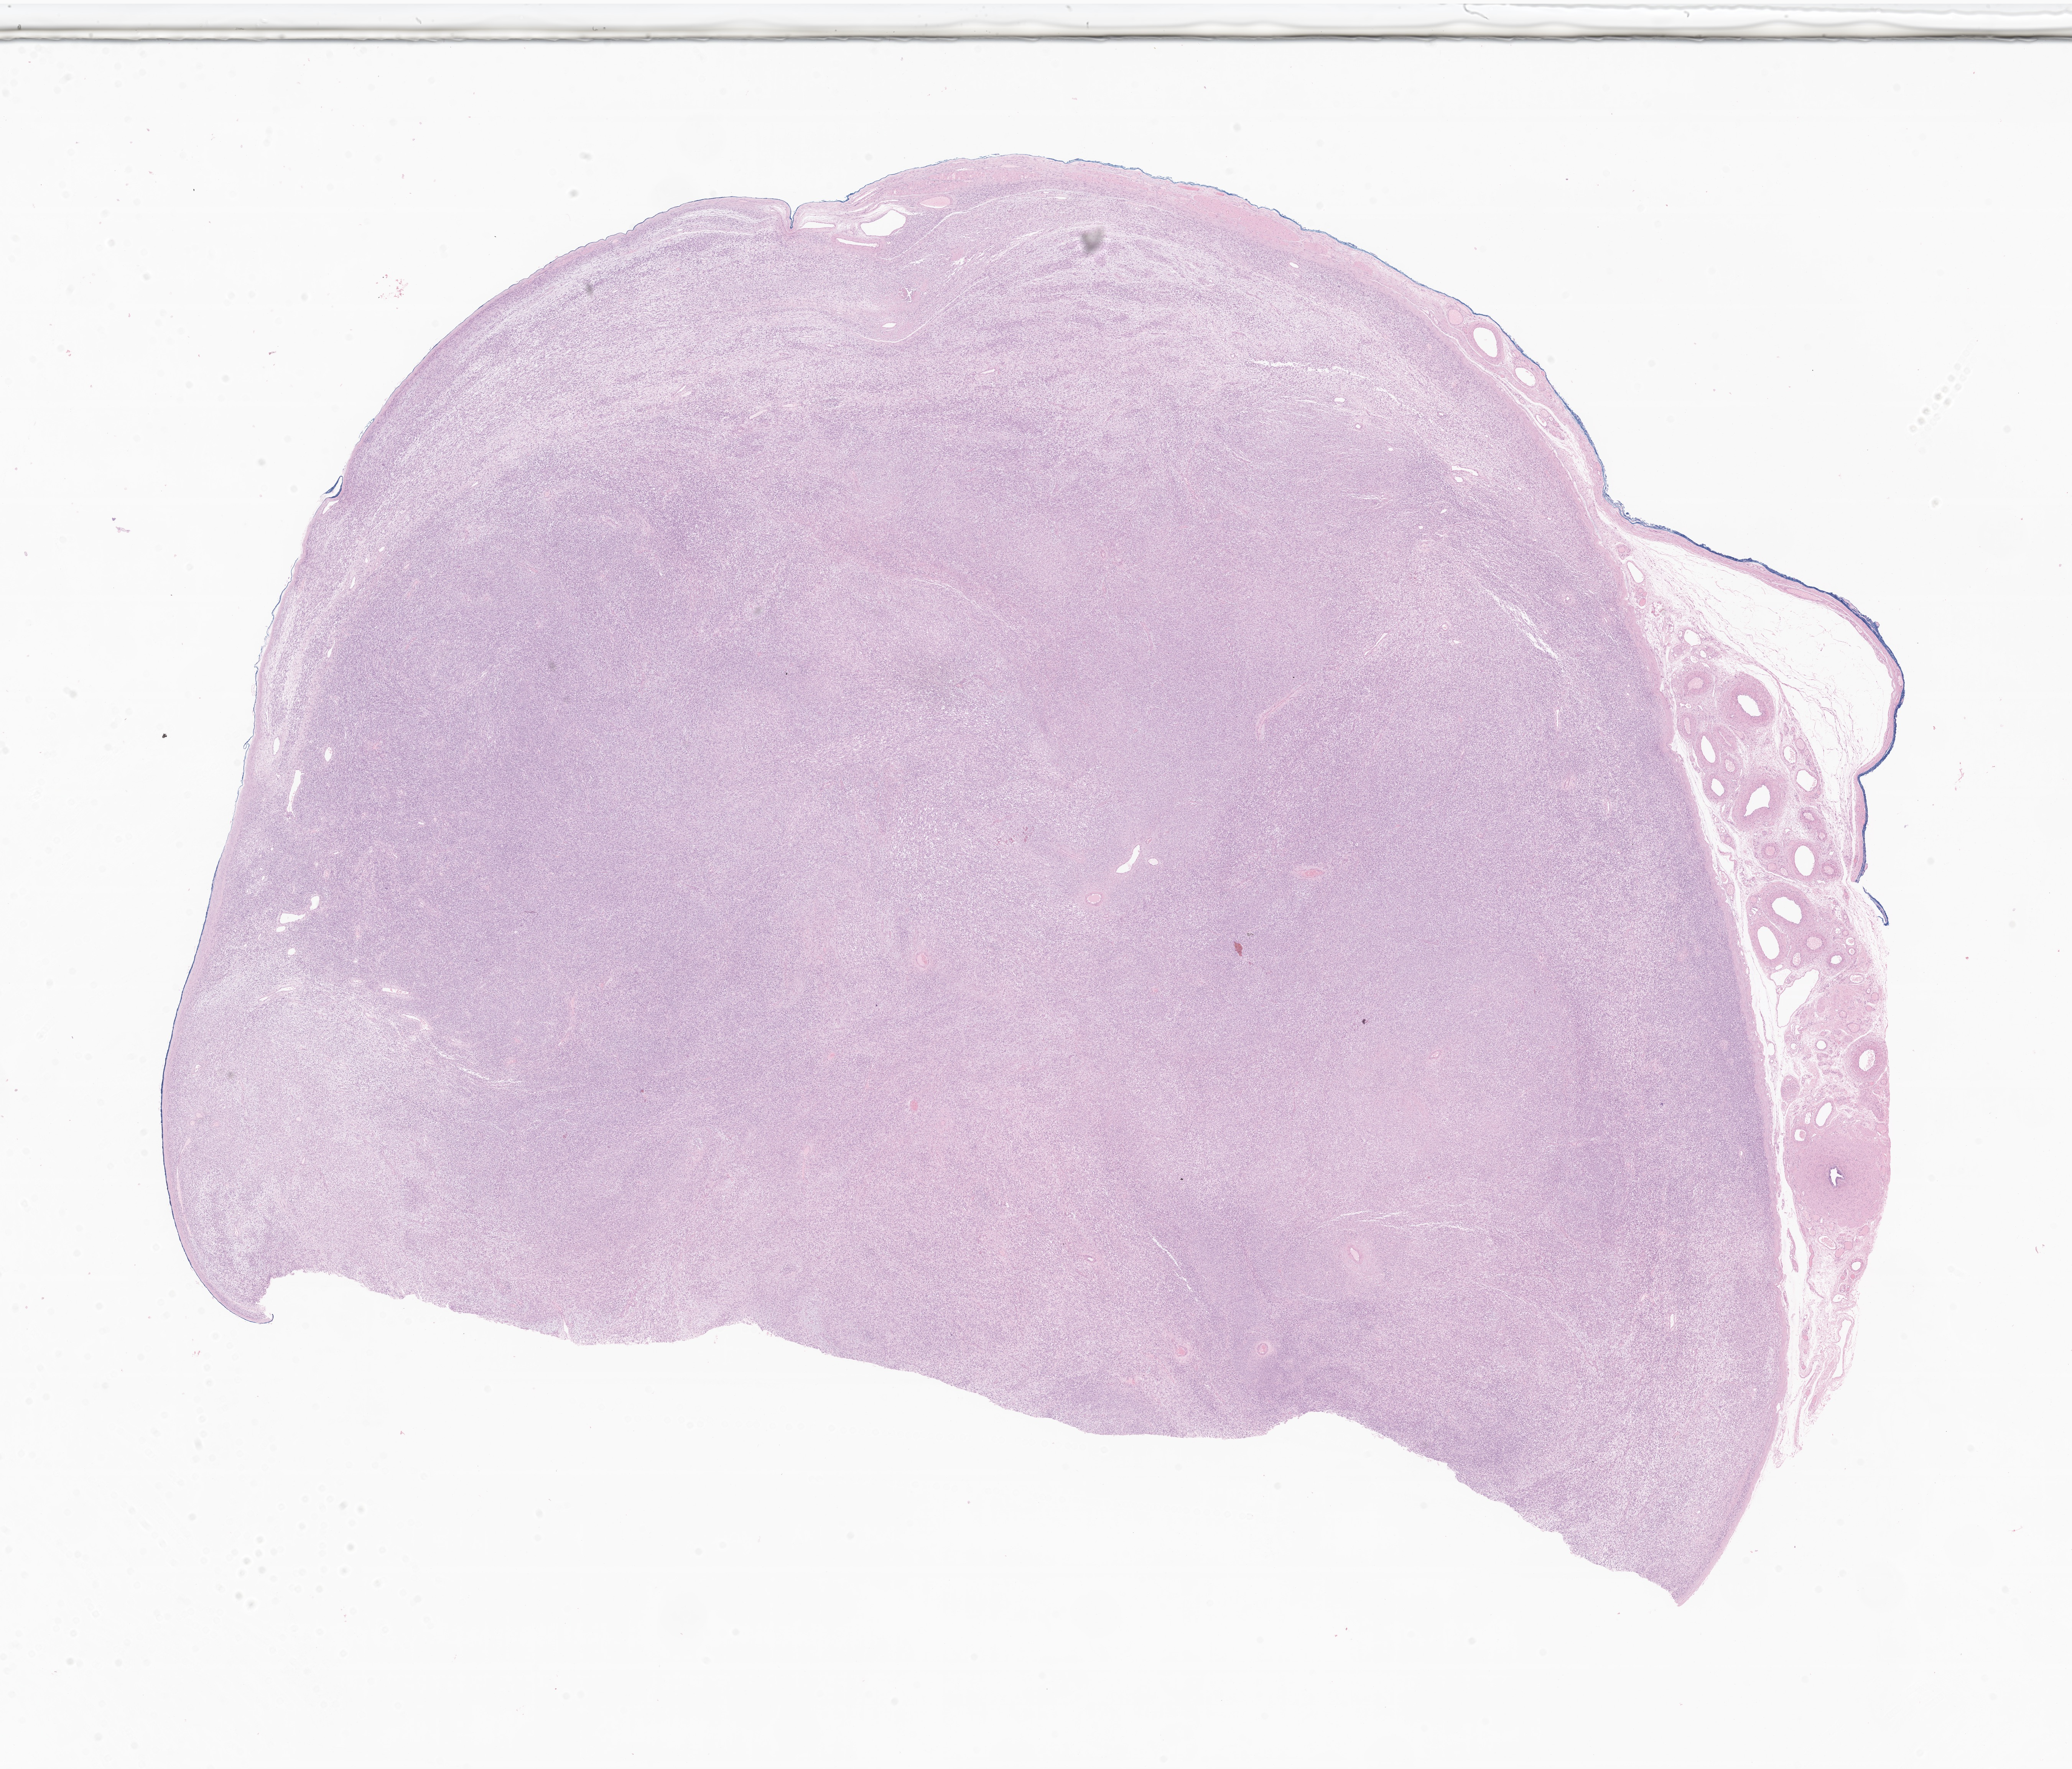
Hematoxylin and eosin (H&E) whole-slide image of tumor tissue from the testis — shown as a low-resolution overview of the whole scanned area (about 22.8 x 19.4 mm). FFPE section. Male patient, age 435 days.
Diagnosis: Embryonal rhabdomyosarcoma, NOS.